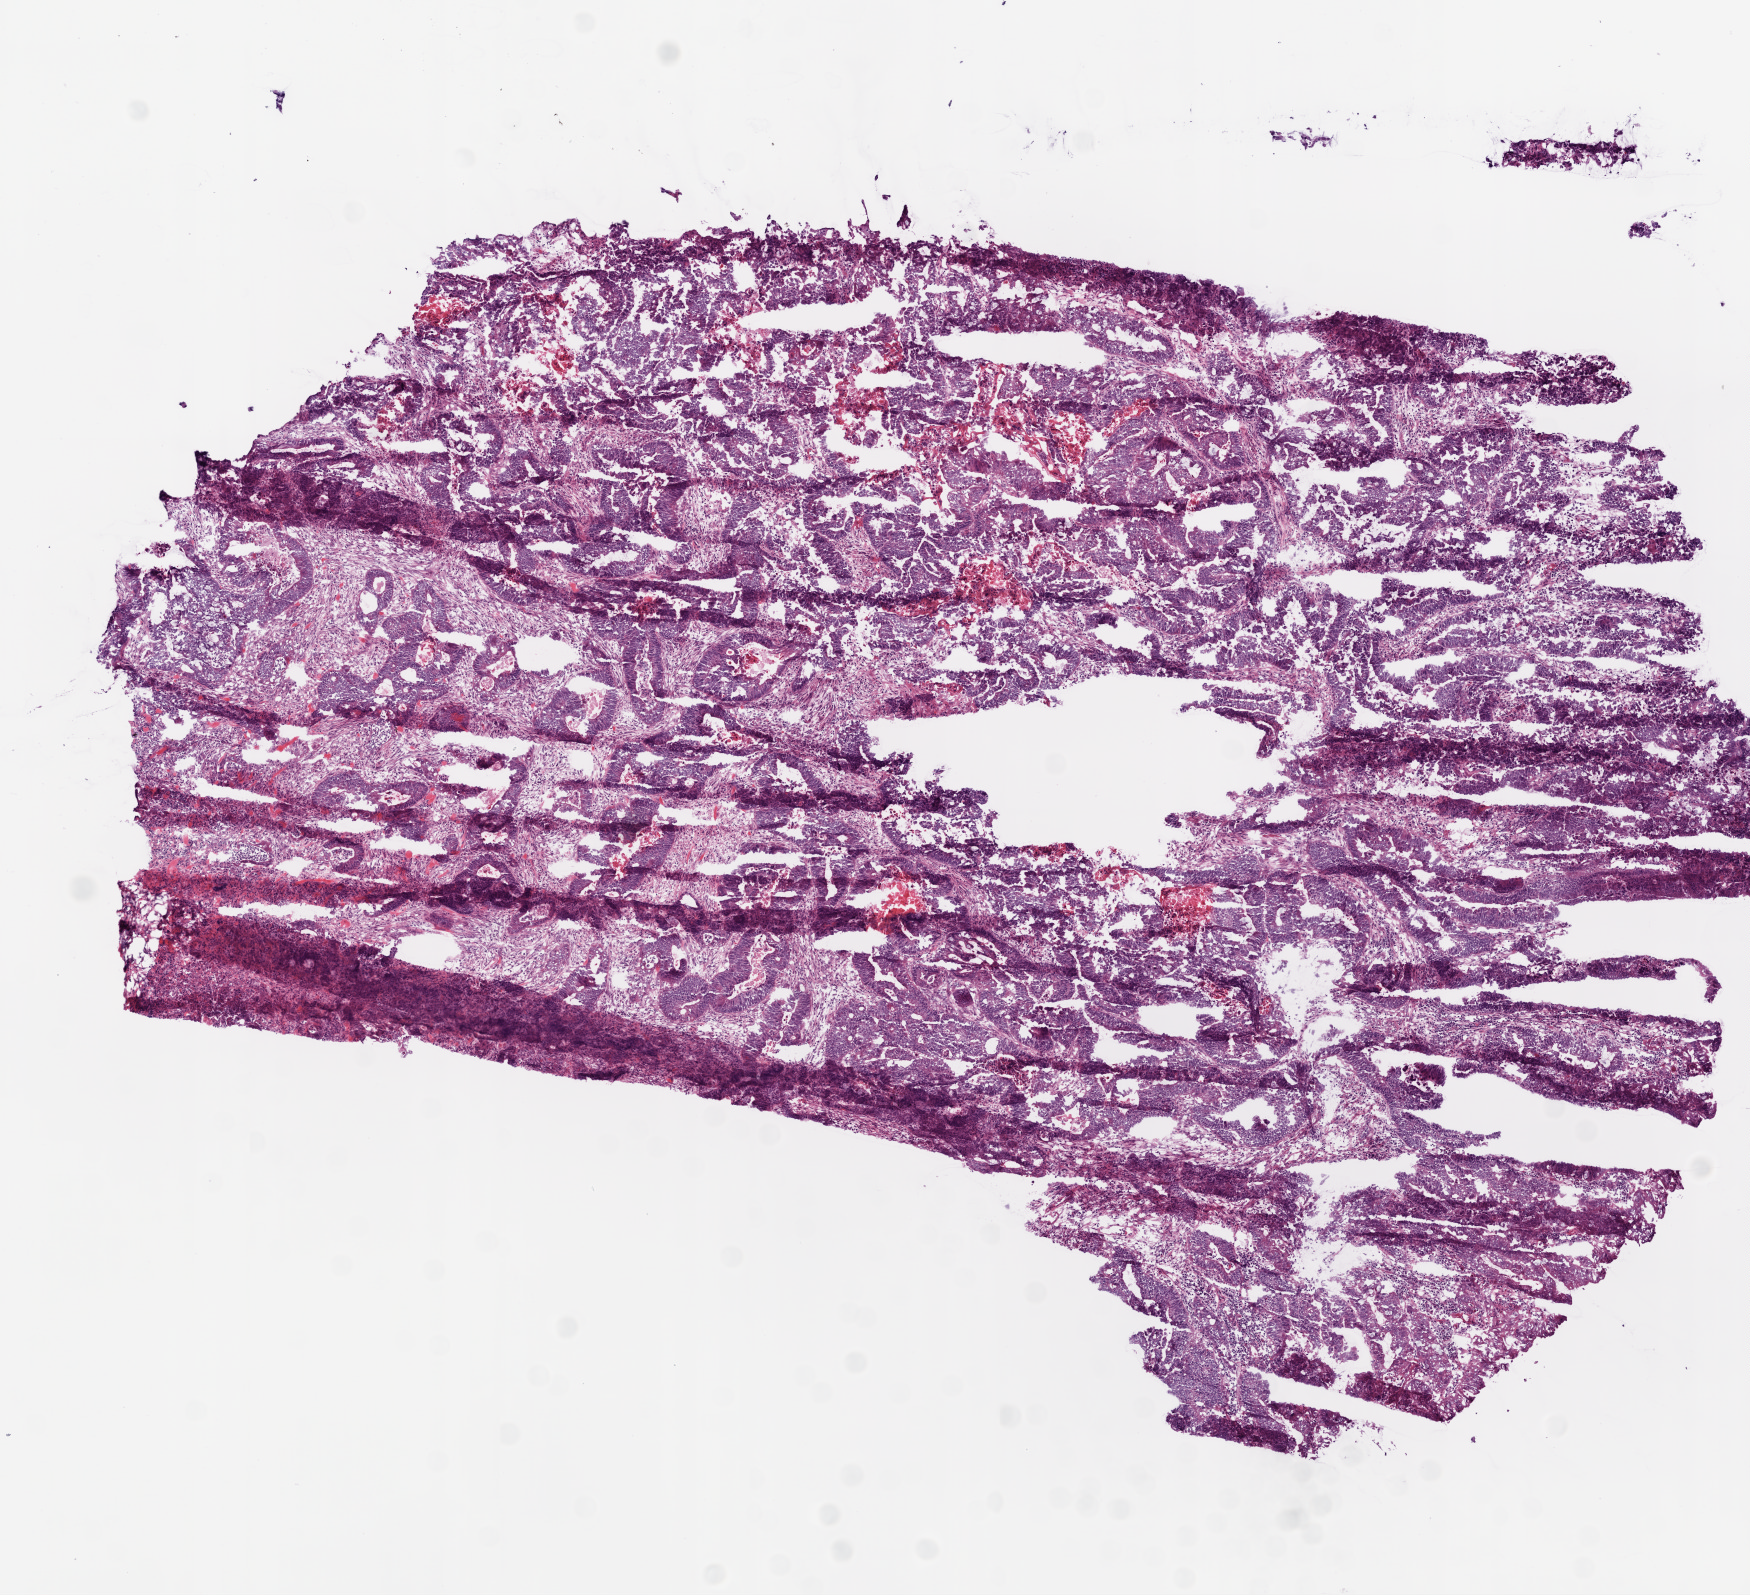
Digitized H&E tissue section (whole slide), low-resolution overview of the scanned area, about 7.0 x 6.4 mm (acquisition: 20x scan); frozen section from the bottom of the tissue portion; primary tumour sample from the colon. Patient: male, age at initial diagnosis 83 years. Composition of this section per pathologist review: tumour cells 60%, tumour nuclei 70%, normal cells 20%, stromal cells 15%, necrosis 5%.
Pathologic diagnosis: Adenocarcinoma, NOS. AJCC pathologic stage: IIA (6th edition).